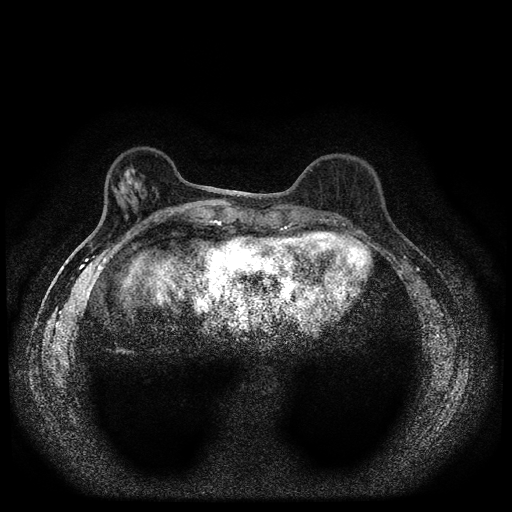
Breast MRI (dynamic contrast-enhanced, multi-phase), one axial slice. Slice 30 of 112 in the series (ordered by position). Dynamic contrast-enhanced series, time point 2 of 5 at this slice position (early post-contrast). 1.5 T. TE 2.7 ms, TR 5.4 ms. 2 mm slice thickness. 512 × 512 image matrix, field of view 320 × 320 mm. Female patient, age 61 years.
Structures marked on this image (semi-automatic segmentation, software-assisted and operator-edited):
- breast lesion (labelled benign in the annotation): box from (x=112, y=169) to (x=141, y=203) px